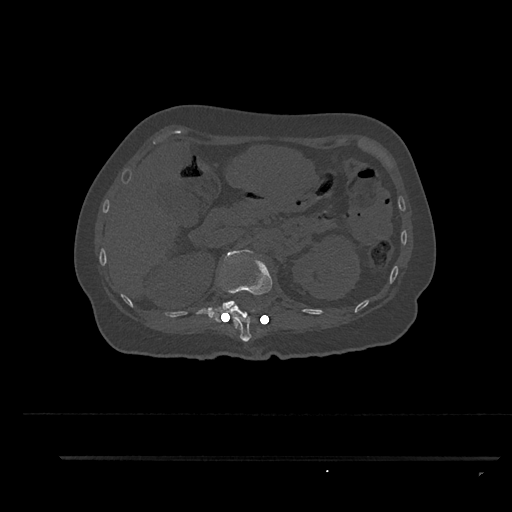
CT including the spine, one axial slice. Slice 240 of 797 in the series (ordered by position). Reconstruction kernel Br40s/3. 120 kVp. Bone window (W 1800 / L 400 HU). 0.5 mm slice thickness. 512 × 512 image matrix, field of view 408 × 408 mm. Patient: female, 44 years. From the clinical record (not read from this slice): primary cancer: renal; vertebrae with lytic lesions (as recorded): L1.
Annotated regions visible in this slice (semi-automatically segmented with operator editing):
- L1 vertebra: bounding box <208,249,253,317> (left, top, right, bottom; pixels)
- T12 vertebra: <209,251,273,342>